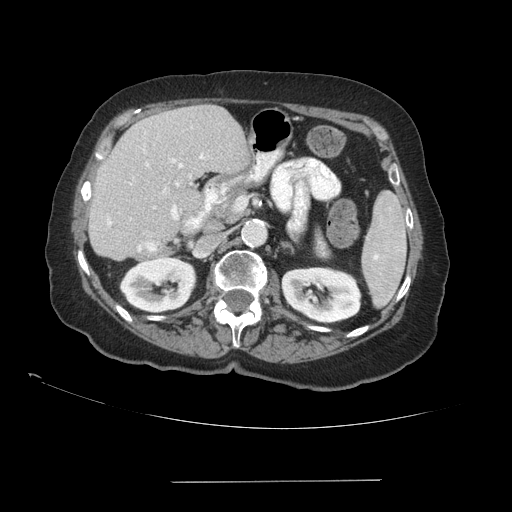
Contrast-enhanced abdominal CT (liver protocol), one axial slice. Slice 48 of 89 in the series (ordered by position). Soft-tissue window (W 400 / L 40 HU). 512 × 512 image matrix. Case-level facts recorded for this patient, not image findings: diagnosis: hepatocellular carcinoma (patient treated with transarterial chemoembolisation; whether this scan precedes or follows treatment is not stated here); TNM stage (as recorded): Stage-IVA; Child-Pugh class: A; tumour differentiation: poorly differentiated.
Annotated regions visible in this slice (semi-automatic segmentation, software-assisted and operator-edited):
- liver parenchyma outside the tumour (the mass and vessels are separate outlines, so this box may not span the whole liver): bounding box (x1, y1, x2, y2) in pixels: (88, 104, 248, 260)
- liver vessels: (107, 154, 204, 252)